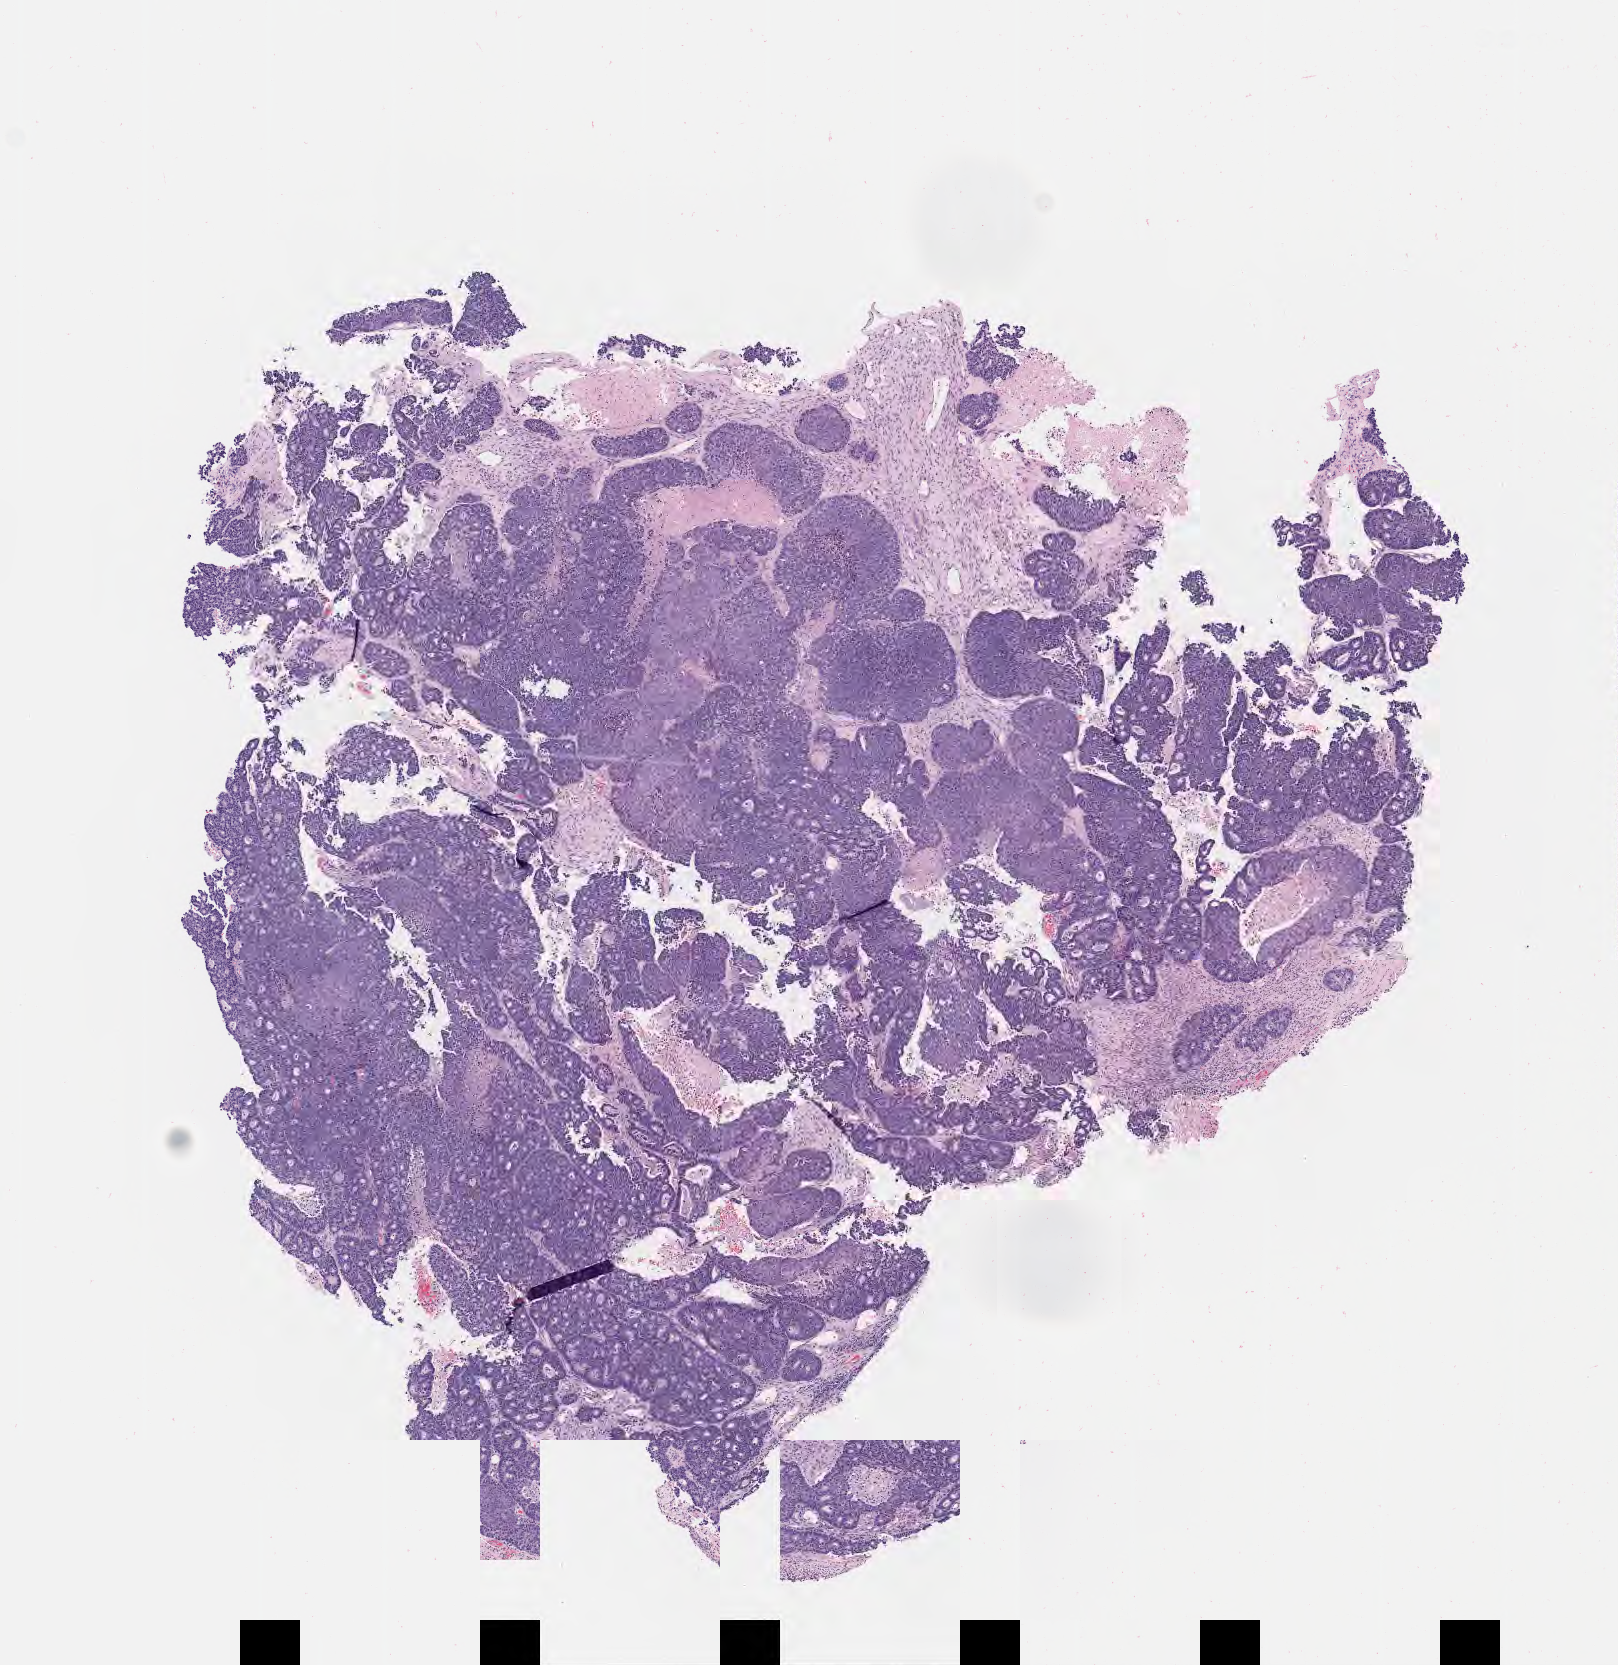
Hematoxylin and eosin (H&E) whole-slide image, a low-resolution overview of the entire scanned area, about 6.5 x 6.7 mm; tumor tissue; anatomic site: cervix. Patient female; aged 48.
- diagnosis: Adenocarcinoma, NOS